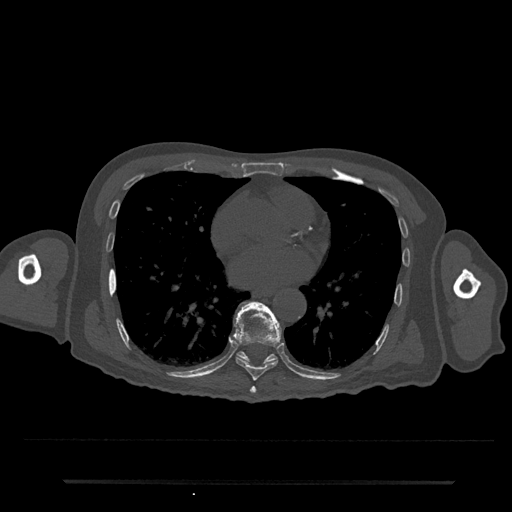
CT including the spine, one axial slice; slice 405 of 797 in the series (ordered by position); reconstruction kernel Br40s/3; 120 kVp; bone window (W 1800 / L 400 HU); 0.5 mm slice thickness; 512 × 512 image matrix, field of view 427 × 427 mm. Male patient, age 74 years. Case-level facts recorded for this patient, not image findings: primary cancer: prostate.
Annotated regions visible in this slice (semi-automatic segmentation, software-assisted and operator-edited):
- T7 vertebra: box from (x=250, y=386) to (x=256, y=394) px
- T8 vertebra: (x=233, y=301)–(x=282, y=381)
- T9 vertebra: (x=237, y=314)–(x=277, y=364)